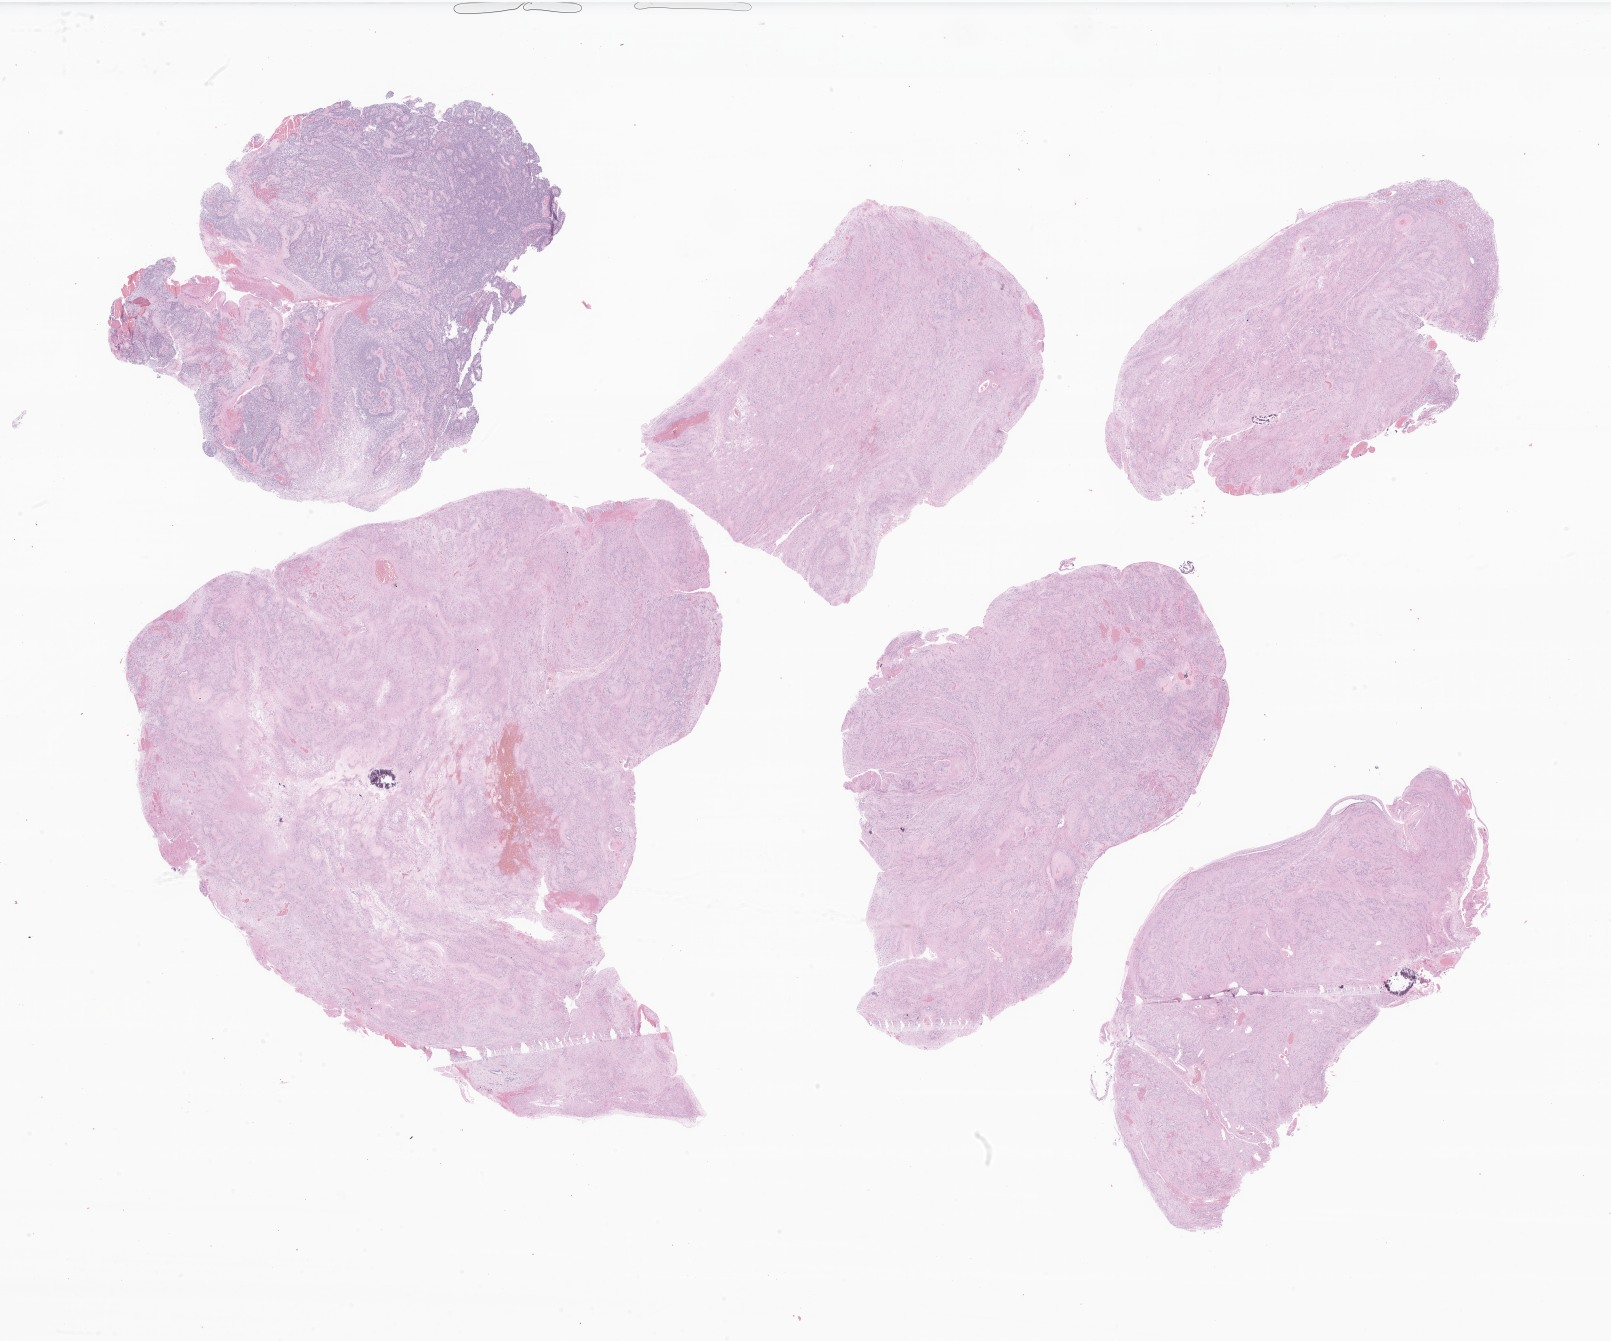
Digitized haematoxylin and eosin-stained section of tumor tissue from the brain — whole scanned area (about 27.2 x 22.6 mm) shown as a low-resolution overview, formalin-fixed, paraffin-embedded (FFPE) tissue. Male patient, age 55 months.
Recorded diagnosis: Ependymoma, NOS.